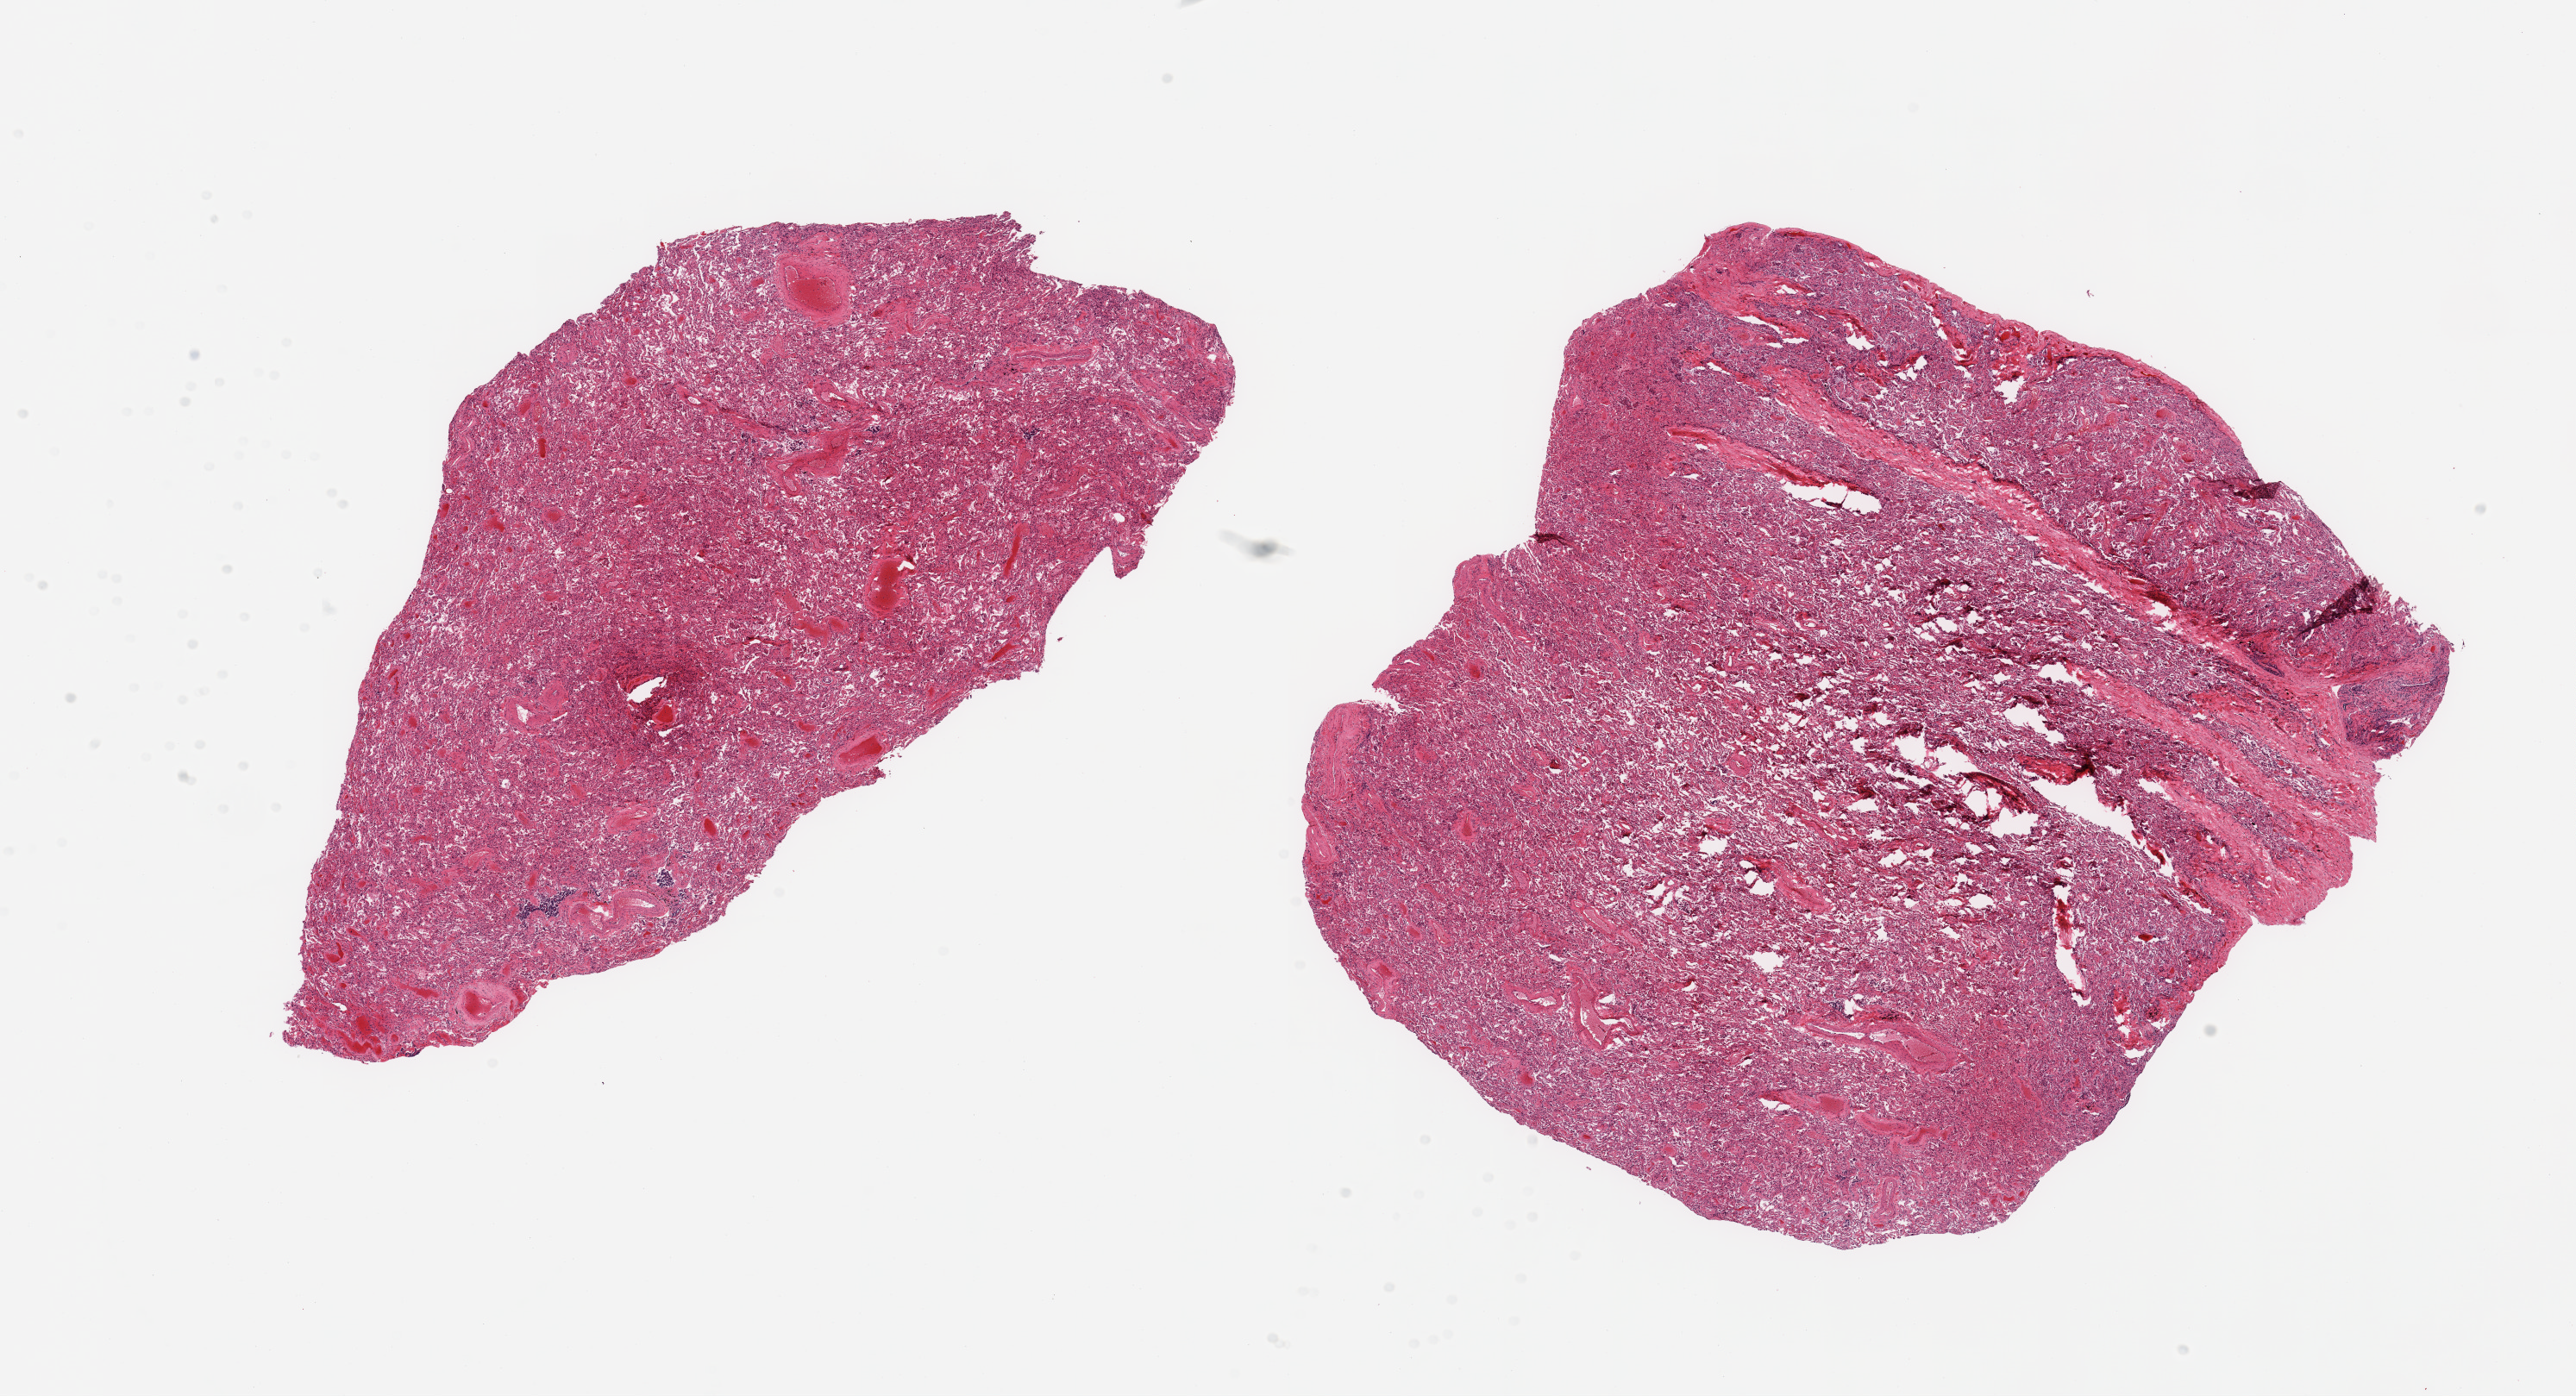
Digitized hematoxylin and eosin (H&E)-stained section, a low-resolution overview of the entire scanned area, about 23.6 x 12.8 mm (slide scanned at 20x). PAXgene-fixed paraffin-embedded (PFPE) section. Sampled site (target tissue): lung. Tissue donor sample.
• pathologist's review note for this sample: 2 pieces; marked congestion; thick walled vessels and thick alveolar septa and collapsed alveoli suggestive of chronic pulmonary hypertension